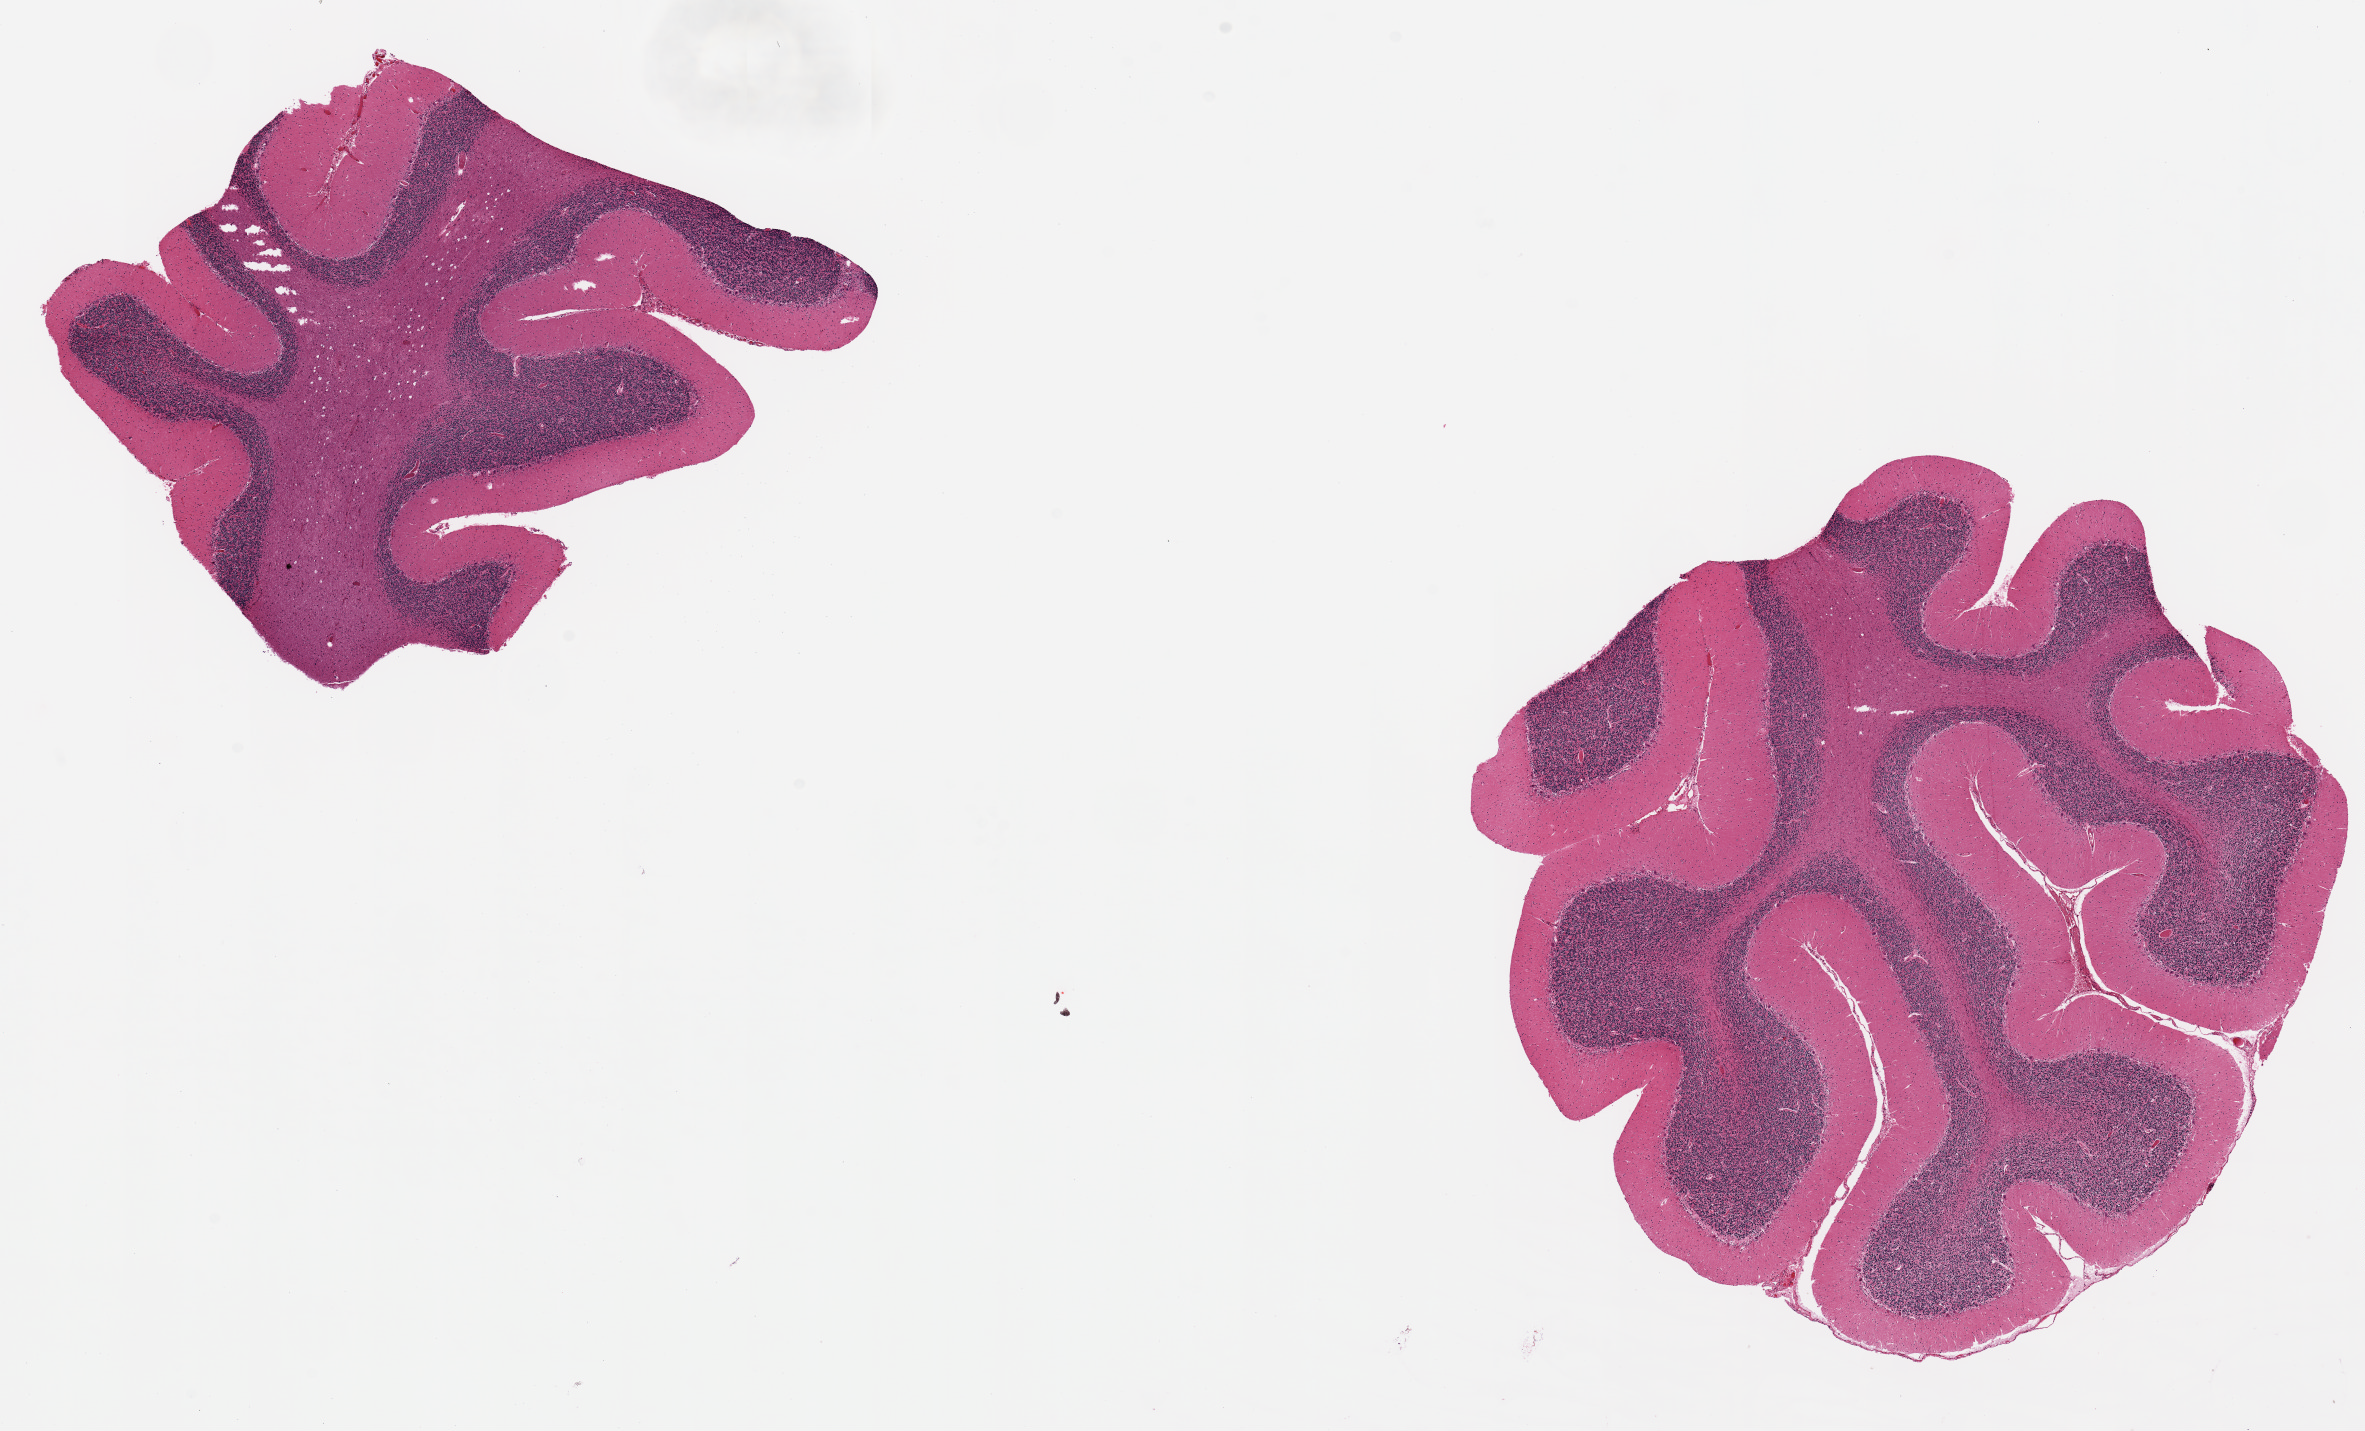
Haematoxylin and eosin whole-slide image, shown as a low-resolution overview of the whole scanned area (about 18.7 x 11.3 mm). PAXgene-fixed, paraffin-embedded tissue. Target tissue: cerebellum. Donor tissue sample.
Reviewer comment on this tissue sample: Two pieces: 6.4x7mm. Slight fractures.